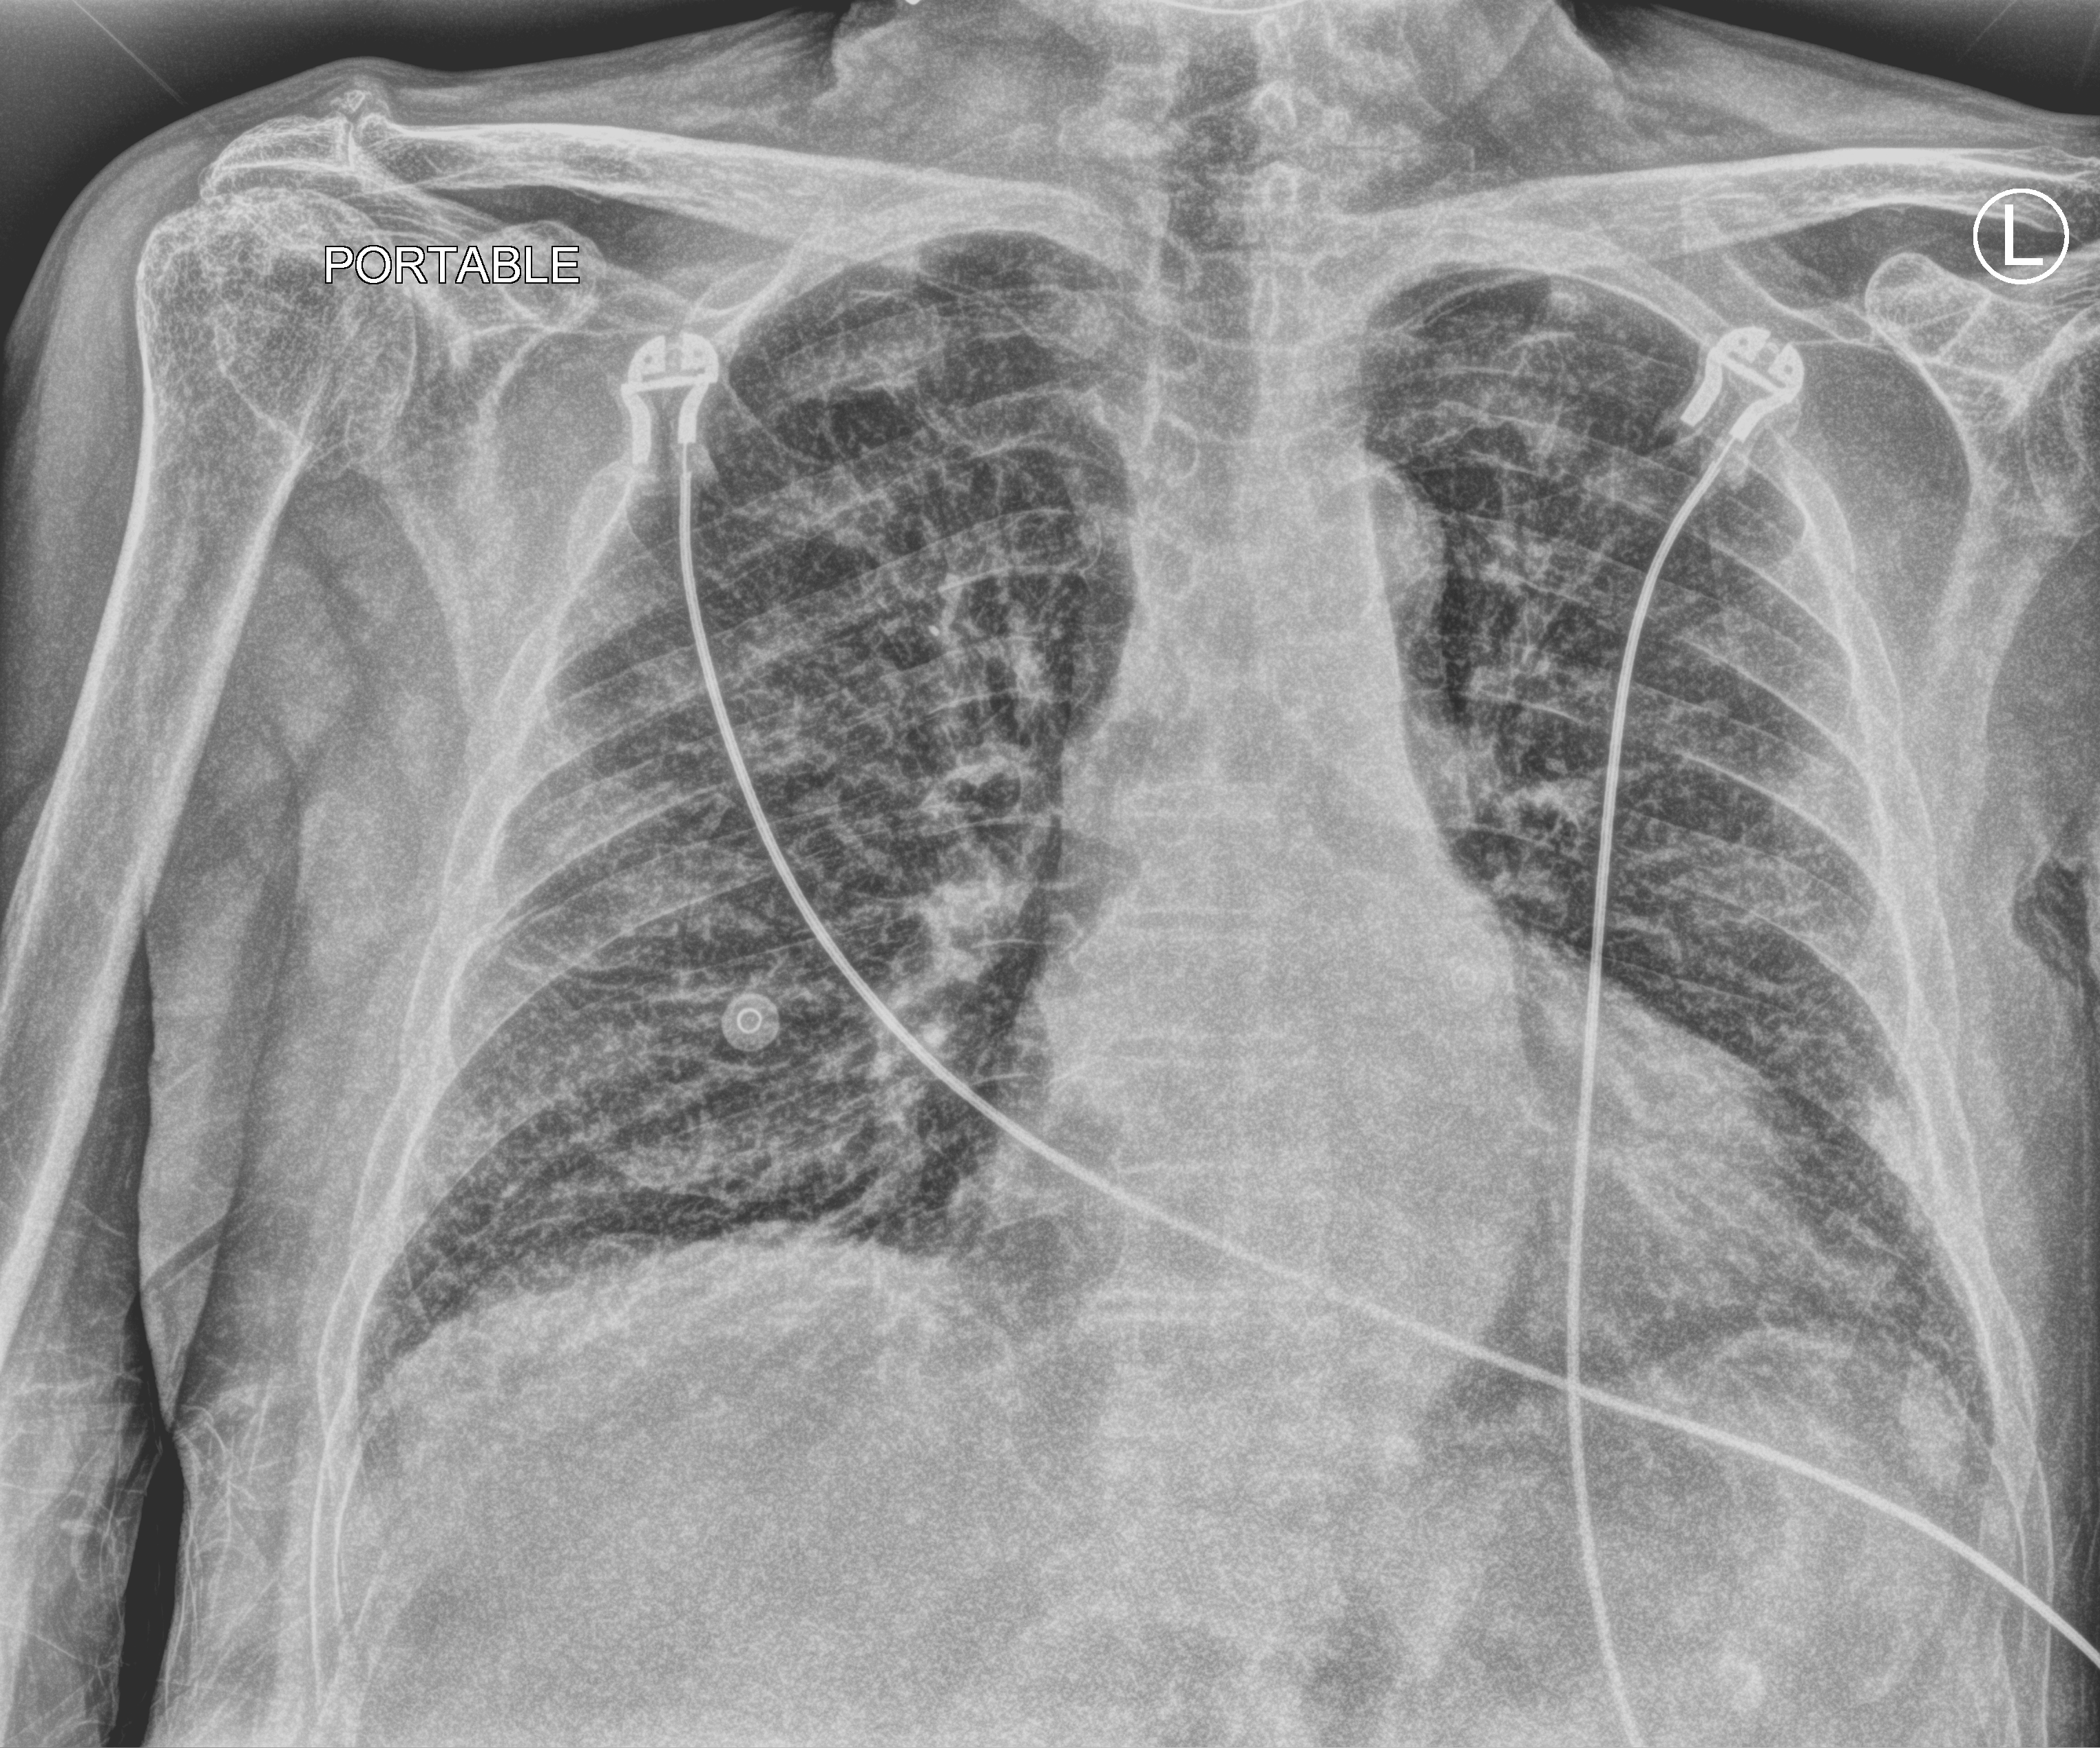
Bedside chest radiograph (computed radiography); anteroposterior (AP) projection. Male patient hospitalised with COVID-19, age 75–90 years.
Admission-level facts for this patient (not findings on this image; timing relative to this image not recorded):
- hypertension (admission record): yes
- admitted to intensive care during this hospital stay: no